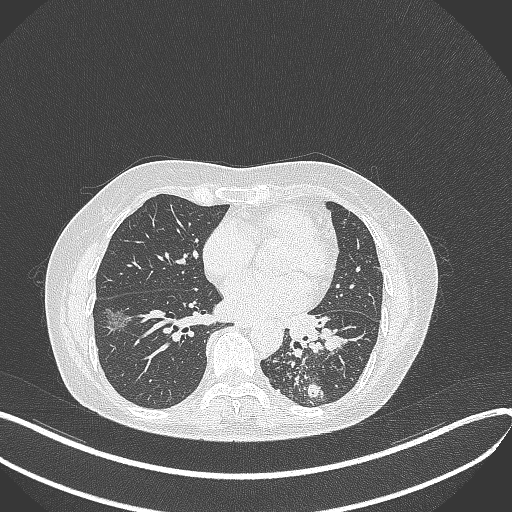
Chest CT, one axial slice; position 172 of 429 along the scan axis; reconstruction kernel B70f; 100 kVp; lung window (W 1500 / L -600 HU); 1 mm slice thickness; 512 × 512 image matrix, field of view 400 × 400 mm. Female patient, age 63 years. From the clinical record (not read from this slice): clinical TNM (as recorded): T1b N0 M0.
Annotated regions visible in this slice (rectangle marked by the reading radiologist):
- lung tumour (recorded histology: adenocarcinoma): bounding box [x1, y1, x2, y2] px = [281, 305, 345, 358]